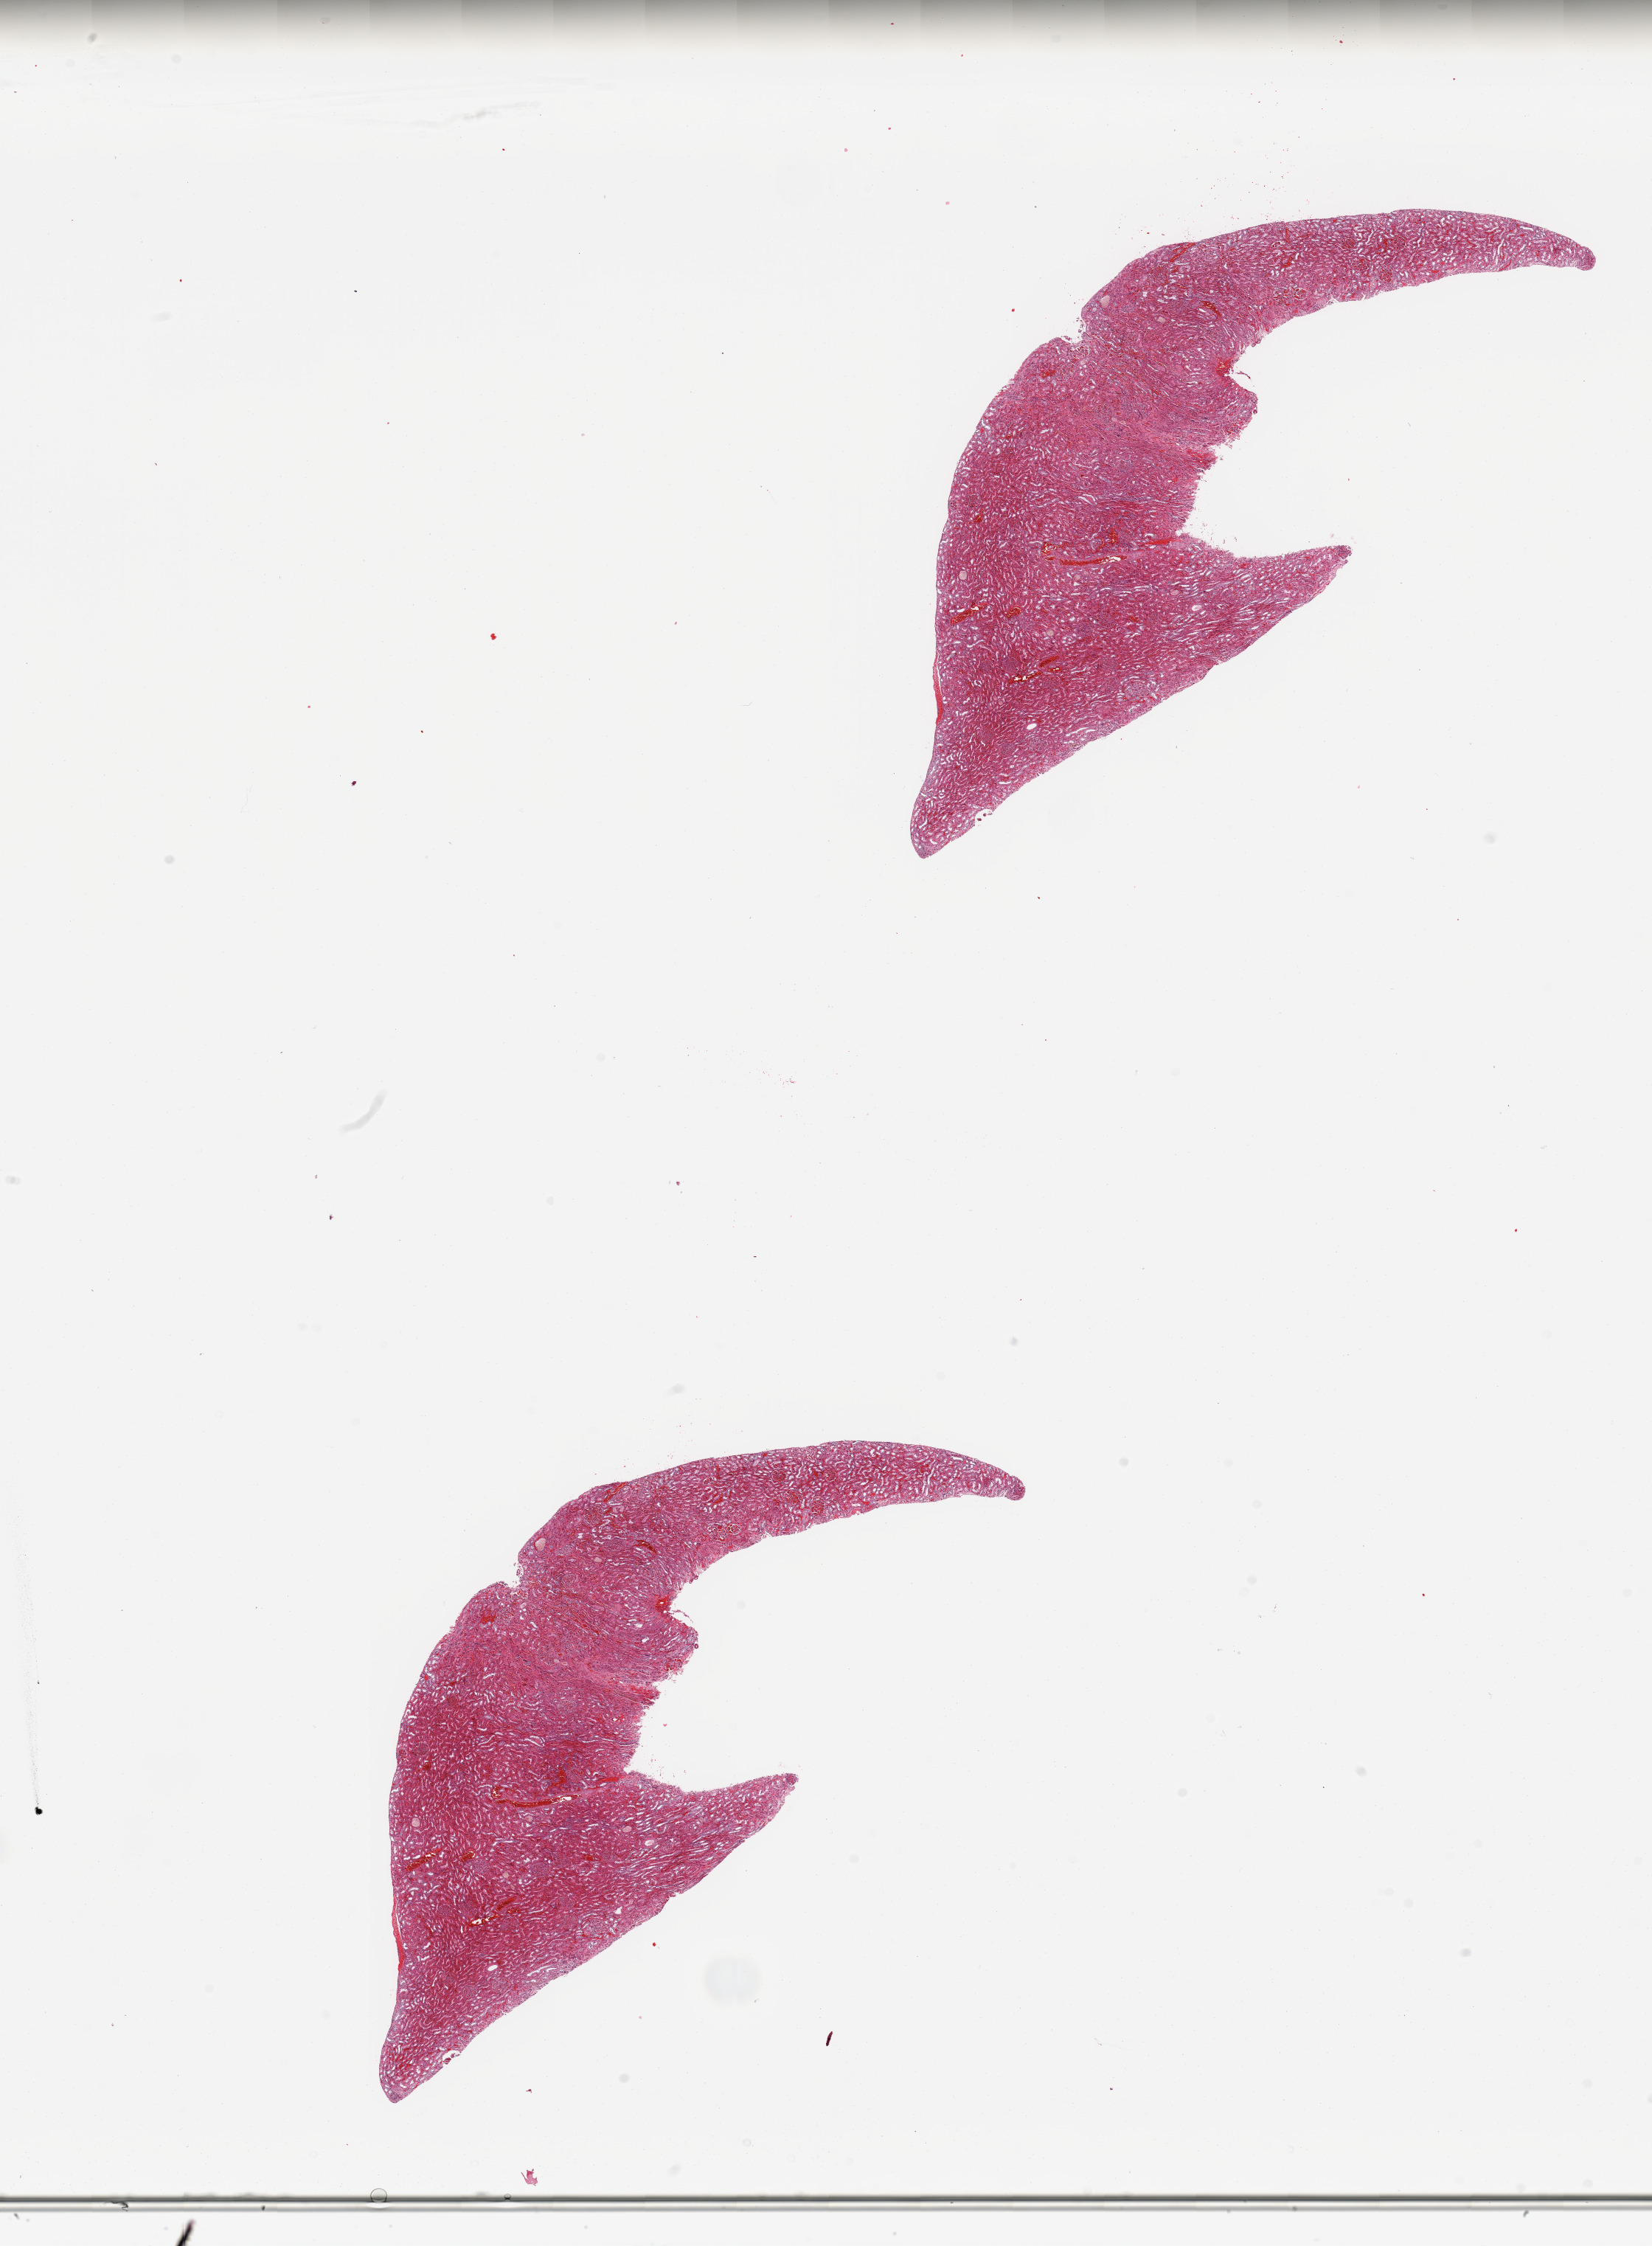
Digitized H&E tissue section (whole slide), a low-resolution overview of the entire scanned area, about 17.7 x 24.1 mm (from a 20x scan). Normal (non-tumour) tissue sample, sampled site: kidney. Patient: male, age 37 years.
This section: normal (non-tumour) tissue from the same patient. Patient diagnosis: Renal cell carcinoma, NOS.